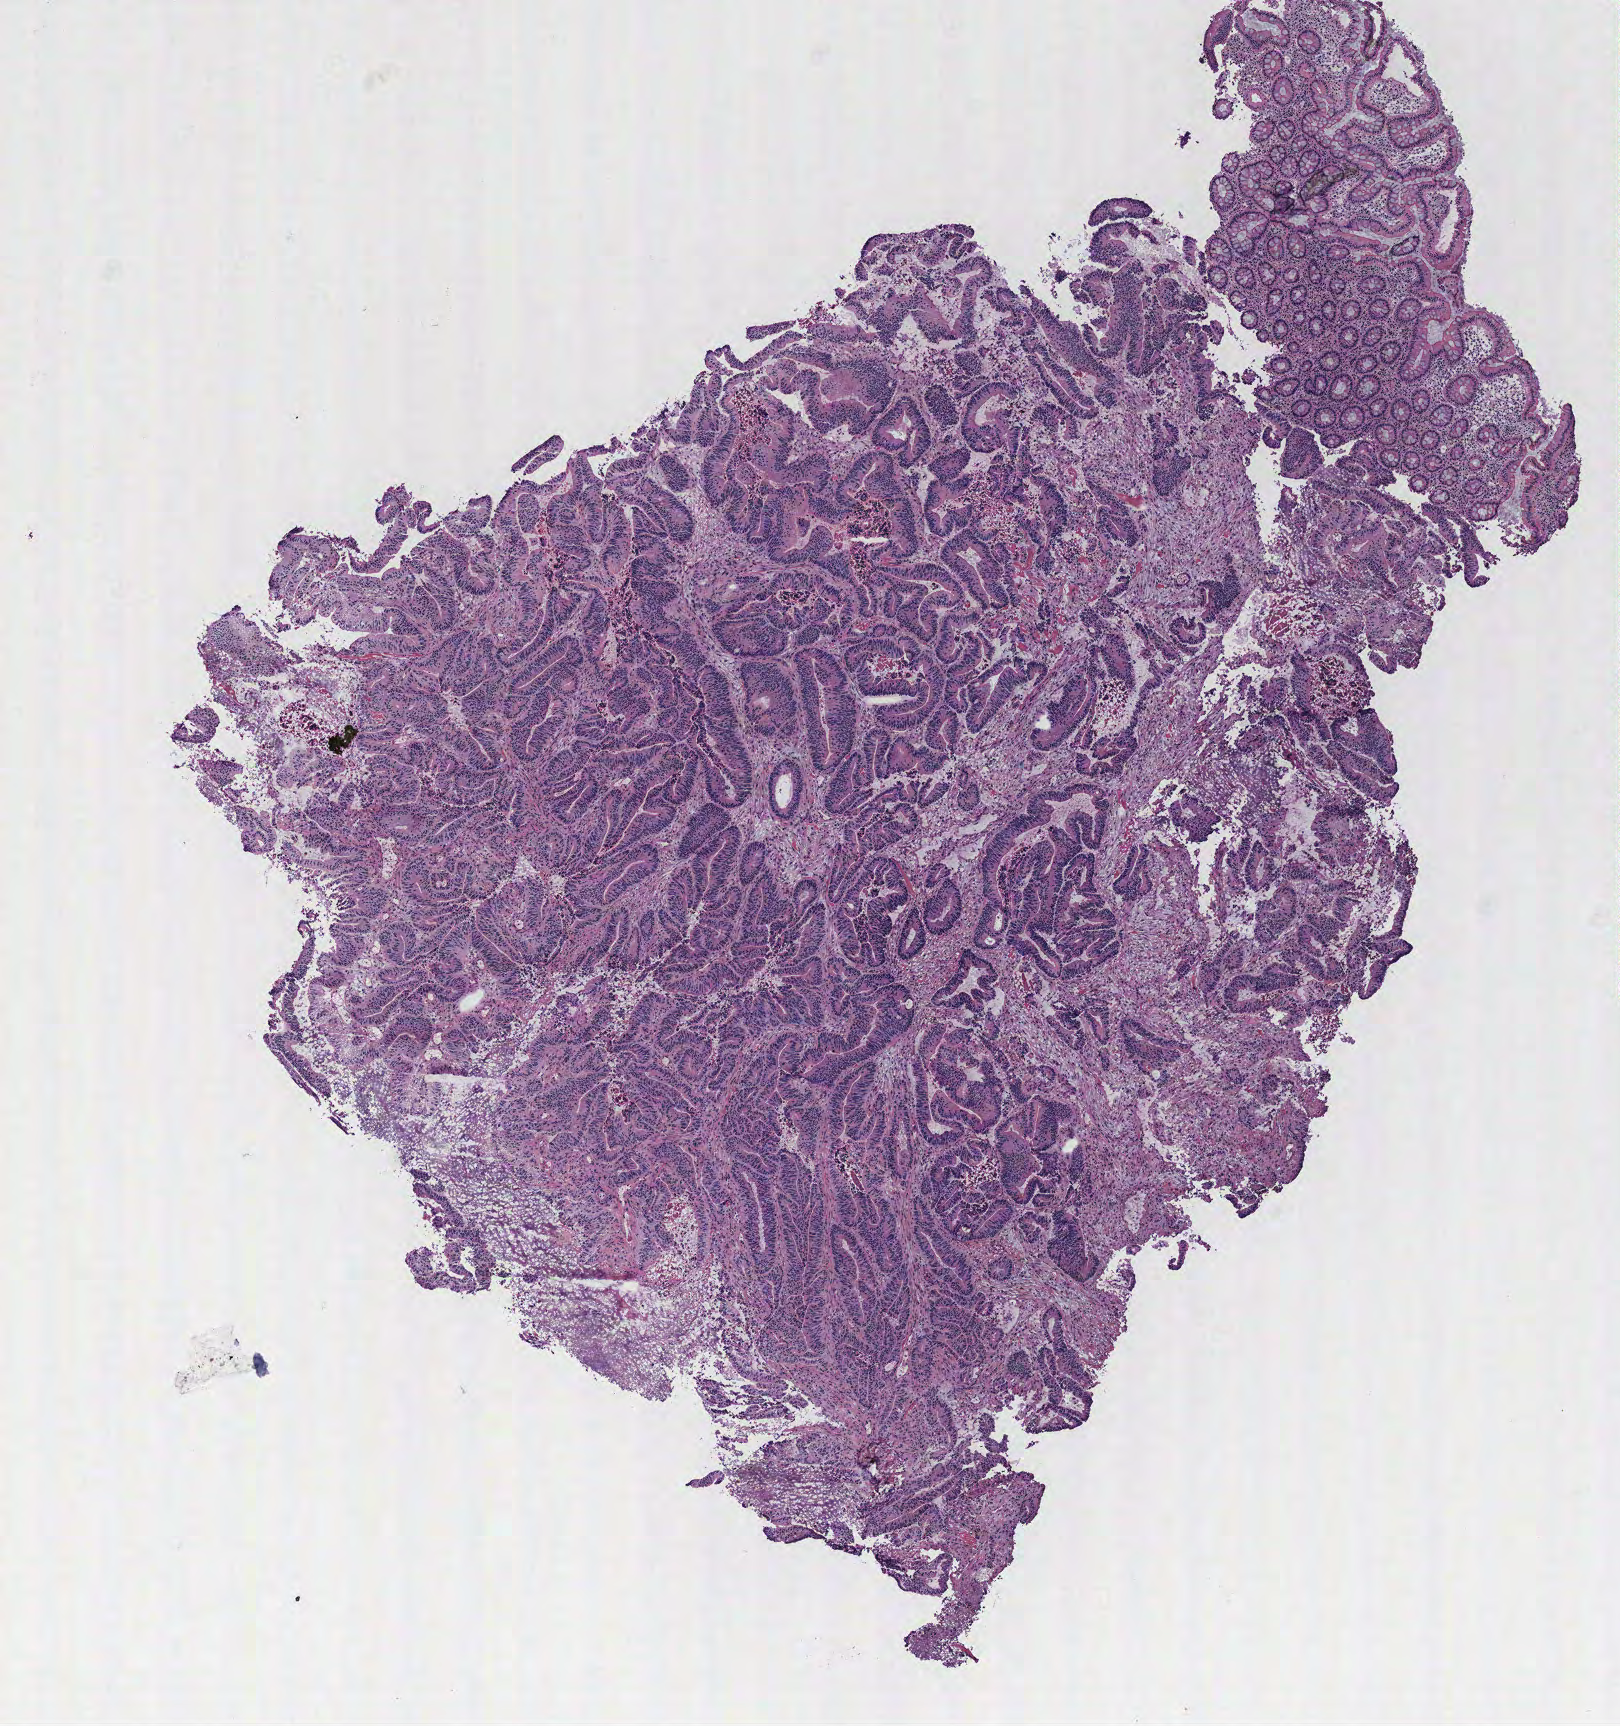
Whole-slide histology image, H&E-stained — a low-resolution overview of the entire scanned area, about 6.5 x 6.9 mm (from a 40x scan). Normal (non-tumour) tissue sample, colon. Male, 58 y/o.
This section: normal (non-tumour) tissue from the same patient. Patient diagnosis (cohort enrolment): colon cancer (colon).